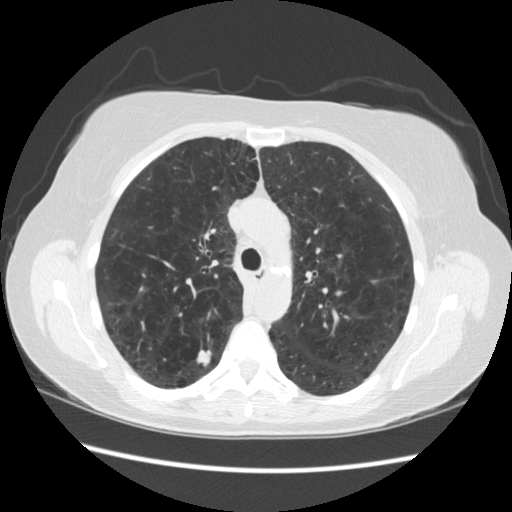
Chest CT (low-dose screening protocol), one axial image, third screening round (two years after baseline), lung window (W 1500 / L -600 HU), standard (soft-tissue) reconstruction kernel (STANDARD), 512 × 512 image matrix. Female, age 55 years at enrolment.
Lesion marked by an expert reader, bounding box [x1, y1, x2, y2] px = [183, 335, 228, 375]. Screening reader's record for this exam (one nodule recorded; not confirmed to be the boxed lesion): non-calcified nodule or mass ≥4 mm, right upper lobe, 11 × 11 mm, poorly defined margins, soft tissue attenuation, pre-existing on the prior screen: no. Participant outcome: lung cancer diagnosed 96 days after this screen — small cell carcinoma, NOS, right upper lobe.